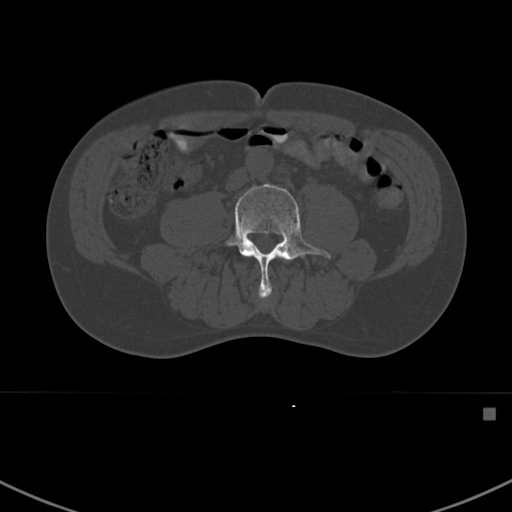
CT including the spine, one axial slice. Slice 243 of 412 in the series (ordered by position). 120 kVp. Bone window (W 1800 / L 400 HU). 1.5 mm slice thickness. 512 × 512 image matrix. Male patient, age 59 years. From the clinical record (not read from this slice): primary cancer: prostate.
Annotated regions visible in this slice (semi-automatic segmentation, software-assisted and operator-edited):
- L3 vertebra: bounding box <260,294,269,300> (left, top, right, bottom; pixels)
- L4 vertebra: <225,183,331,299>